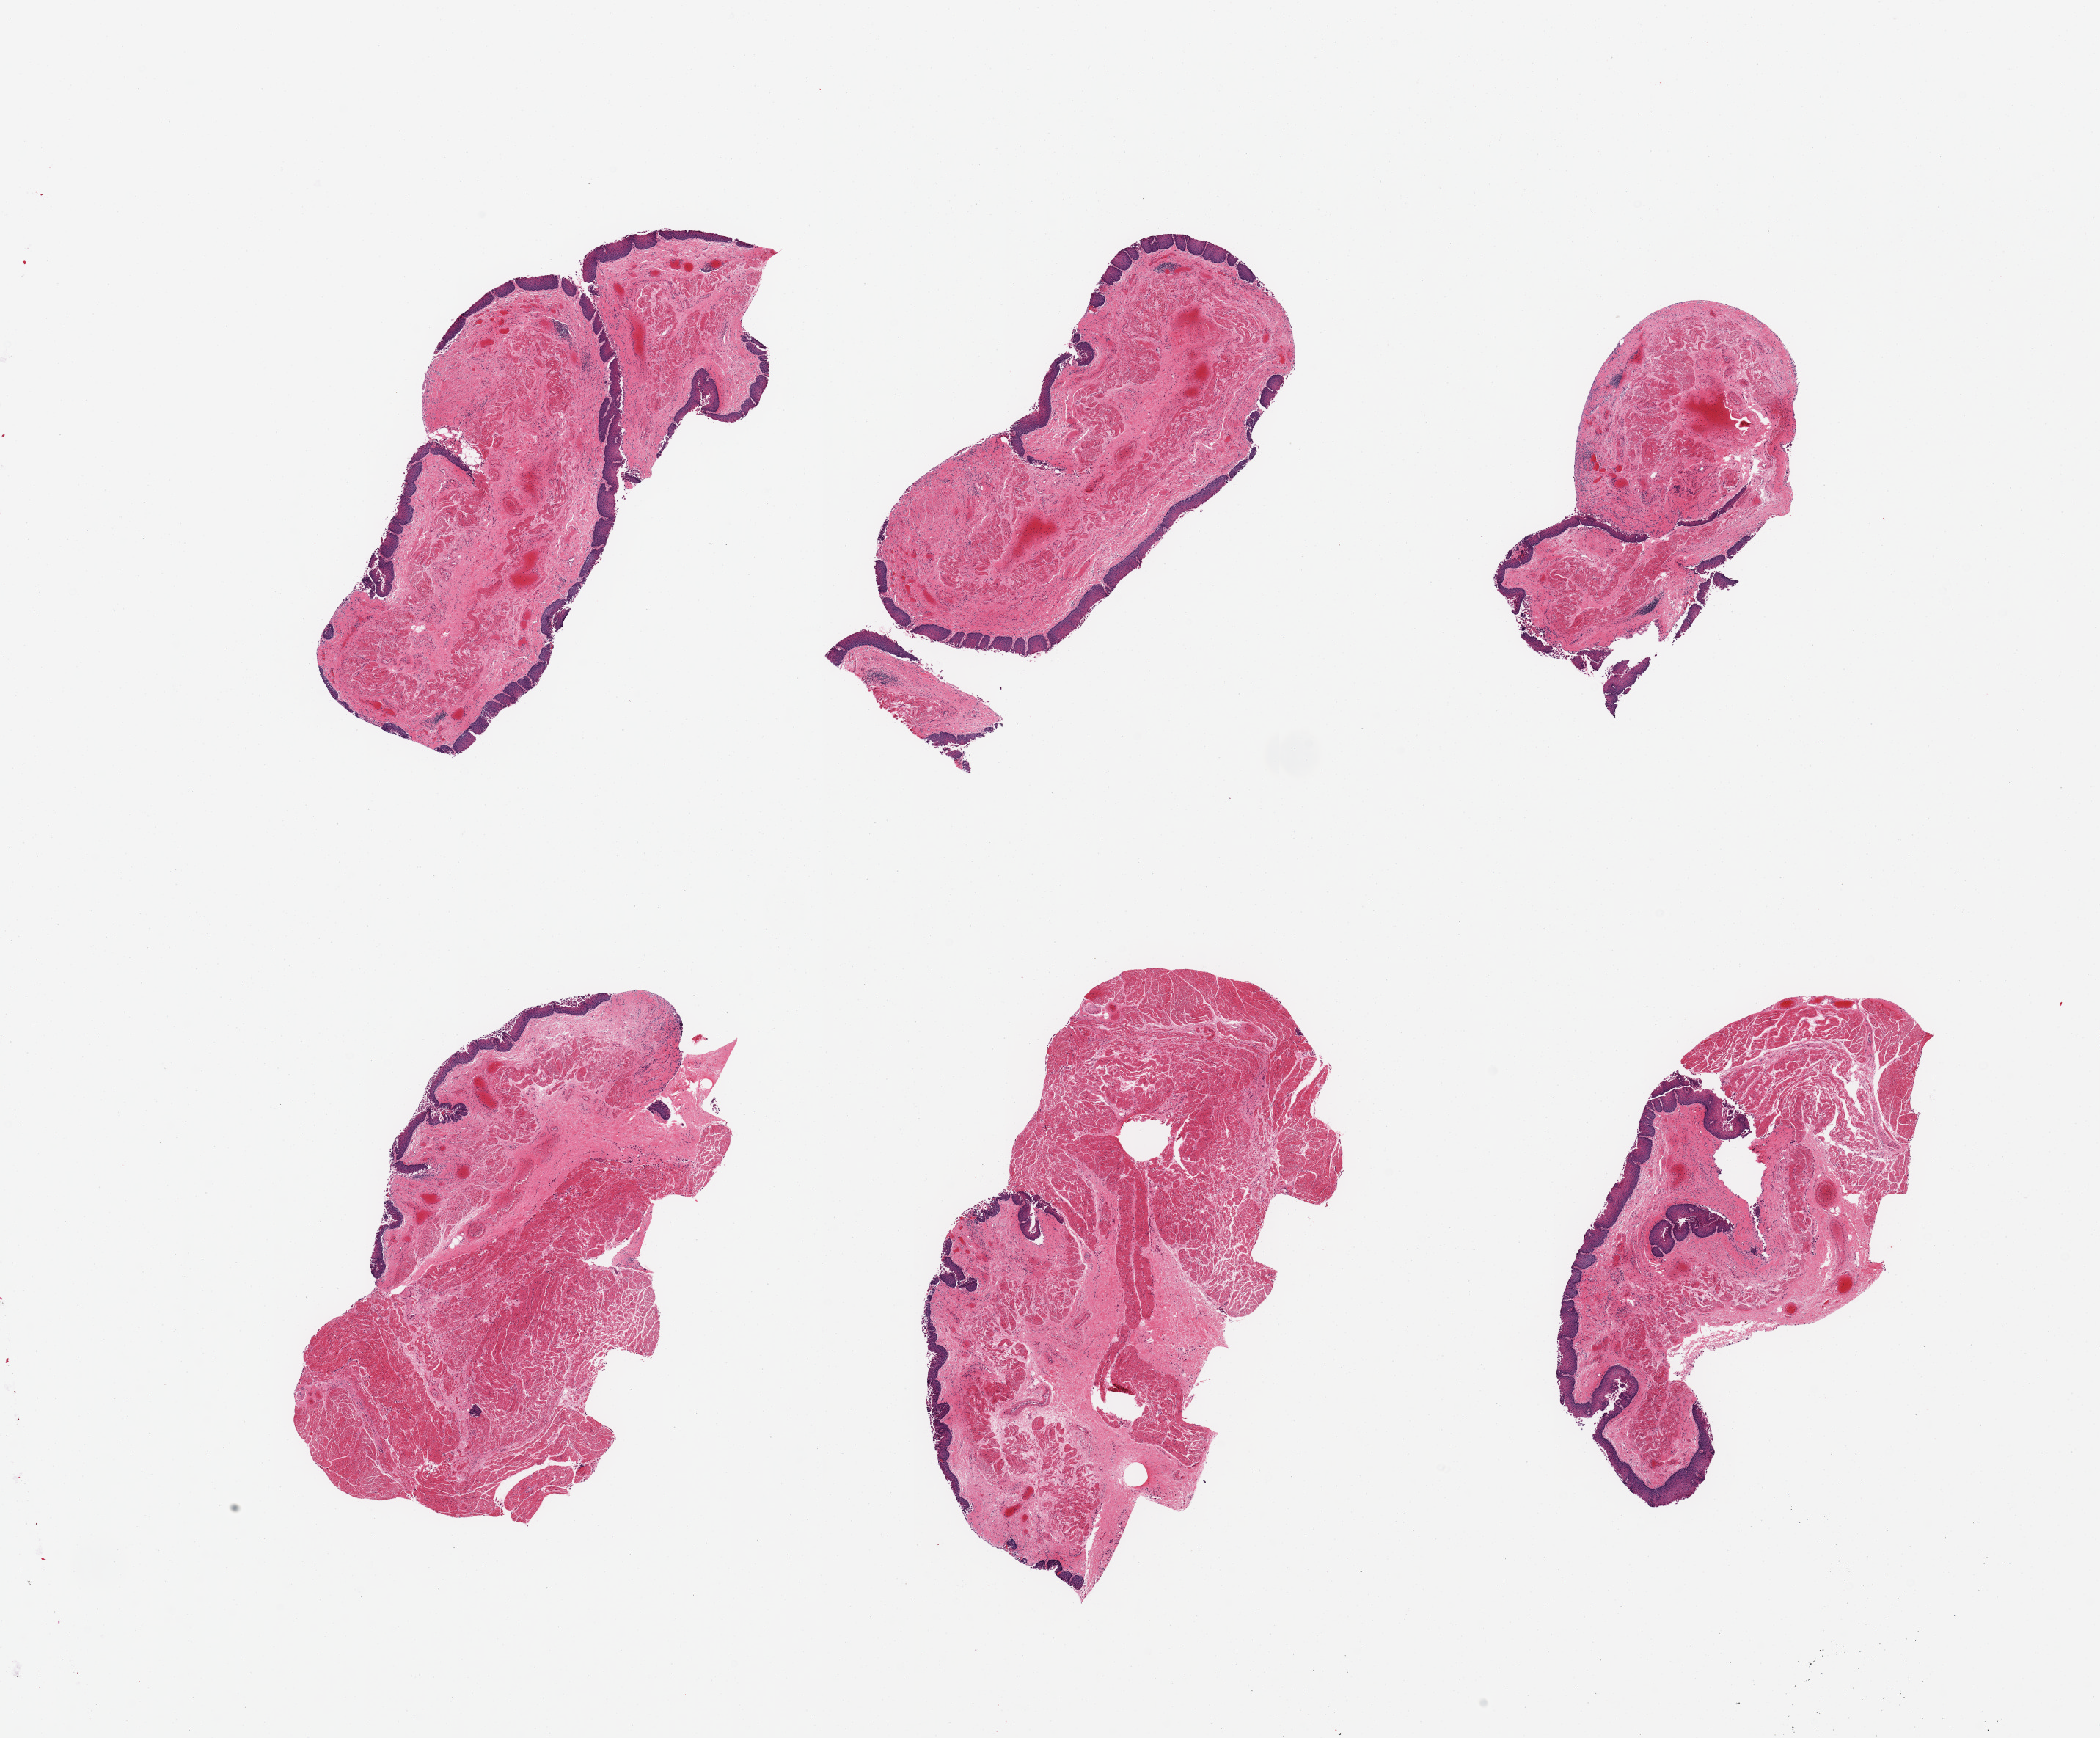
Whole-slide image, H&E stain, a low-resolution overview of the entire scanned area, about 22.6 x 18.7 mm. PAXgene-fixed paraffin-embedded (PFPE) section. Target tissue: esophageal mucous membrane. Tissue donor sample. Donor sex: male.
Pathologist's review note for this sample: 6 pieces, target squamous mucosa up to ~0.15mm, sloughing, moderately advanced autolysis.